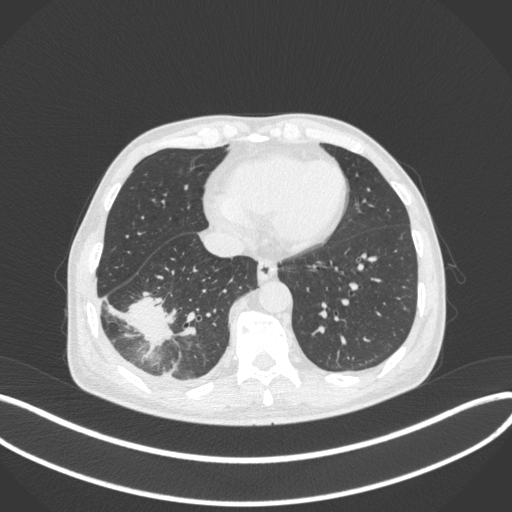
Chest CT, one axial slice; slice 112 of 385 in the series (ordered by position); reconstruction kernel B31f; 120 kVp; lung window (W 1500 / L -600 HU); 512 × 512 image matrix, field of view 400 × 400 mm. Patient: male, 64 years. From the clinical record (not read from this slice): clinical TNM (as recorded): T3 N0 M0; histopathological grade: G2-3.
Outlined on this slice (bounding box drawn by a radiologist):
- lung tumour (recorded histology: adenocarcinoma): bounding box <127,292,180,356> (left, top, right, bottom; pixels)